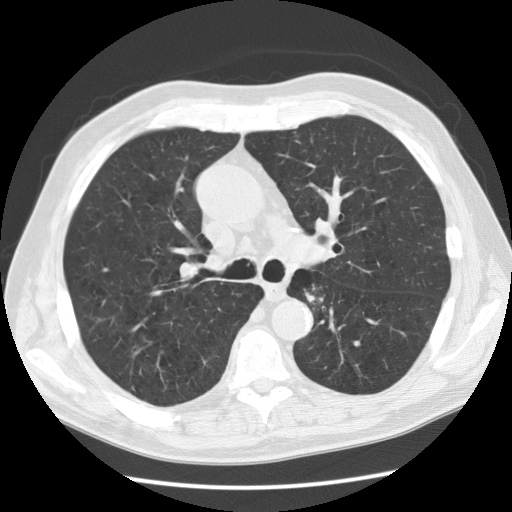
Low-dose screening chest CT, one axial slice; position 83 of 130 along the scan axis; reconstruction kernel STANDARD; 120 kVp; lung window (W 1500 / L -600 HU); 2.5 mm slice thickness; 512 × 512 image matrix.
Annotated regions visible in this slice (manually delineated by an expert):
- lesion 1 (tumor, lower lobe of left lung): bounding box <305,284,329,305> (left, top, right, bottom; pixels)